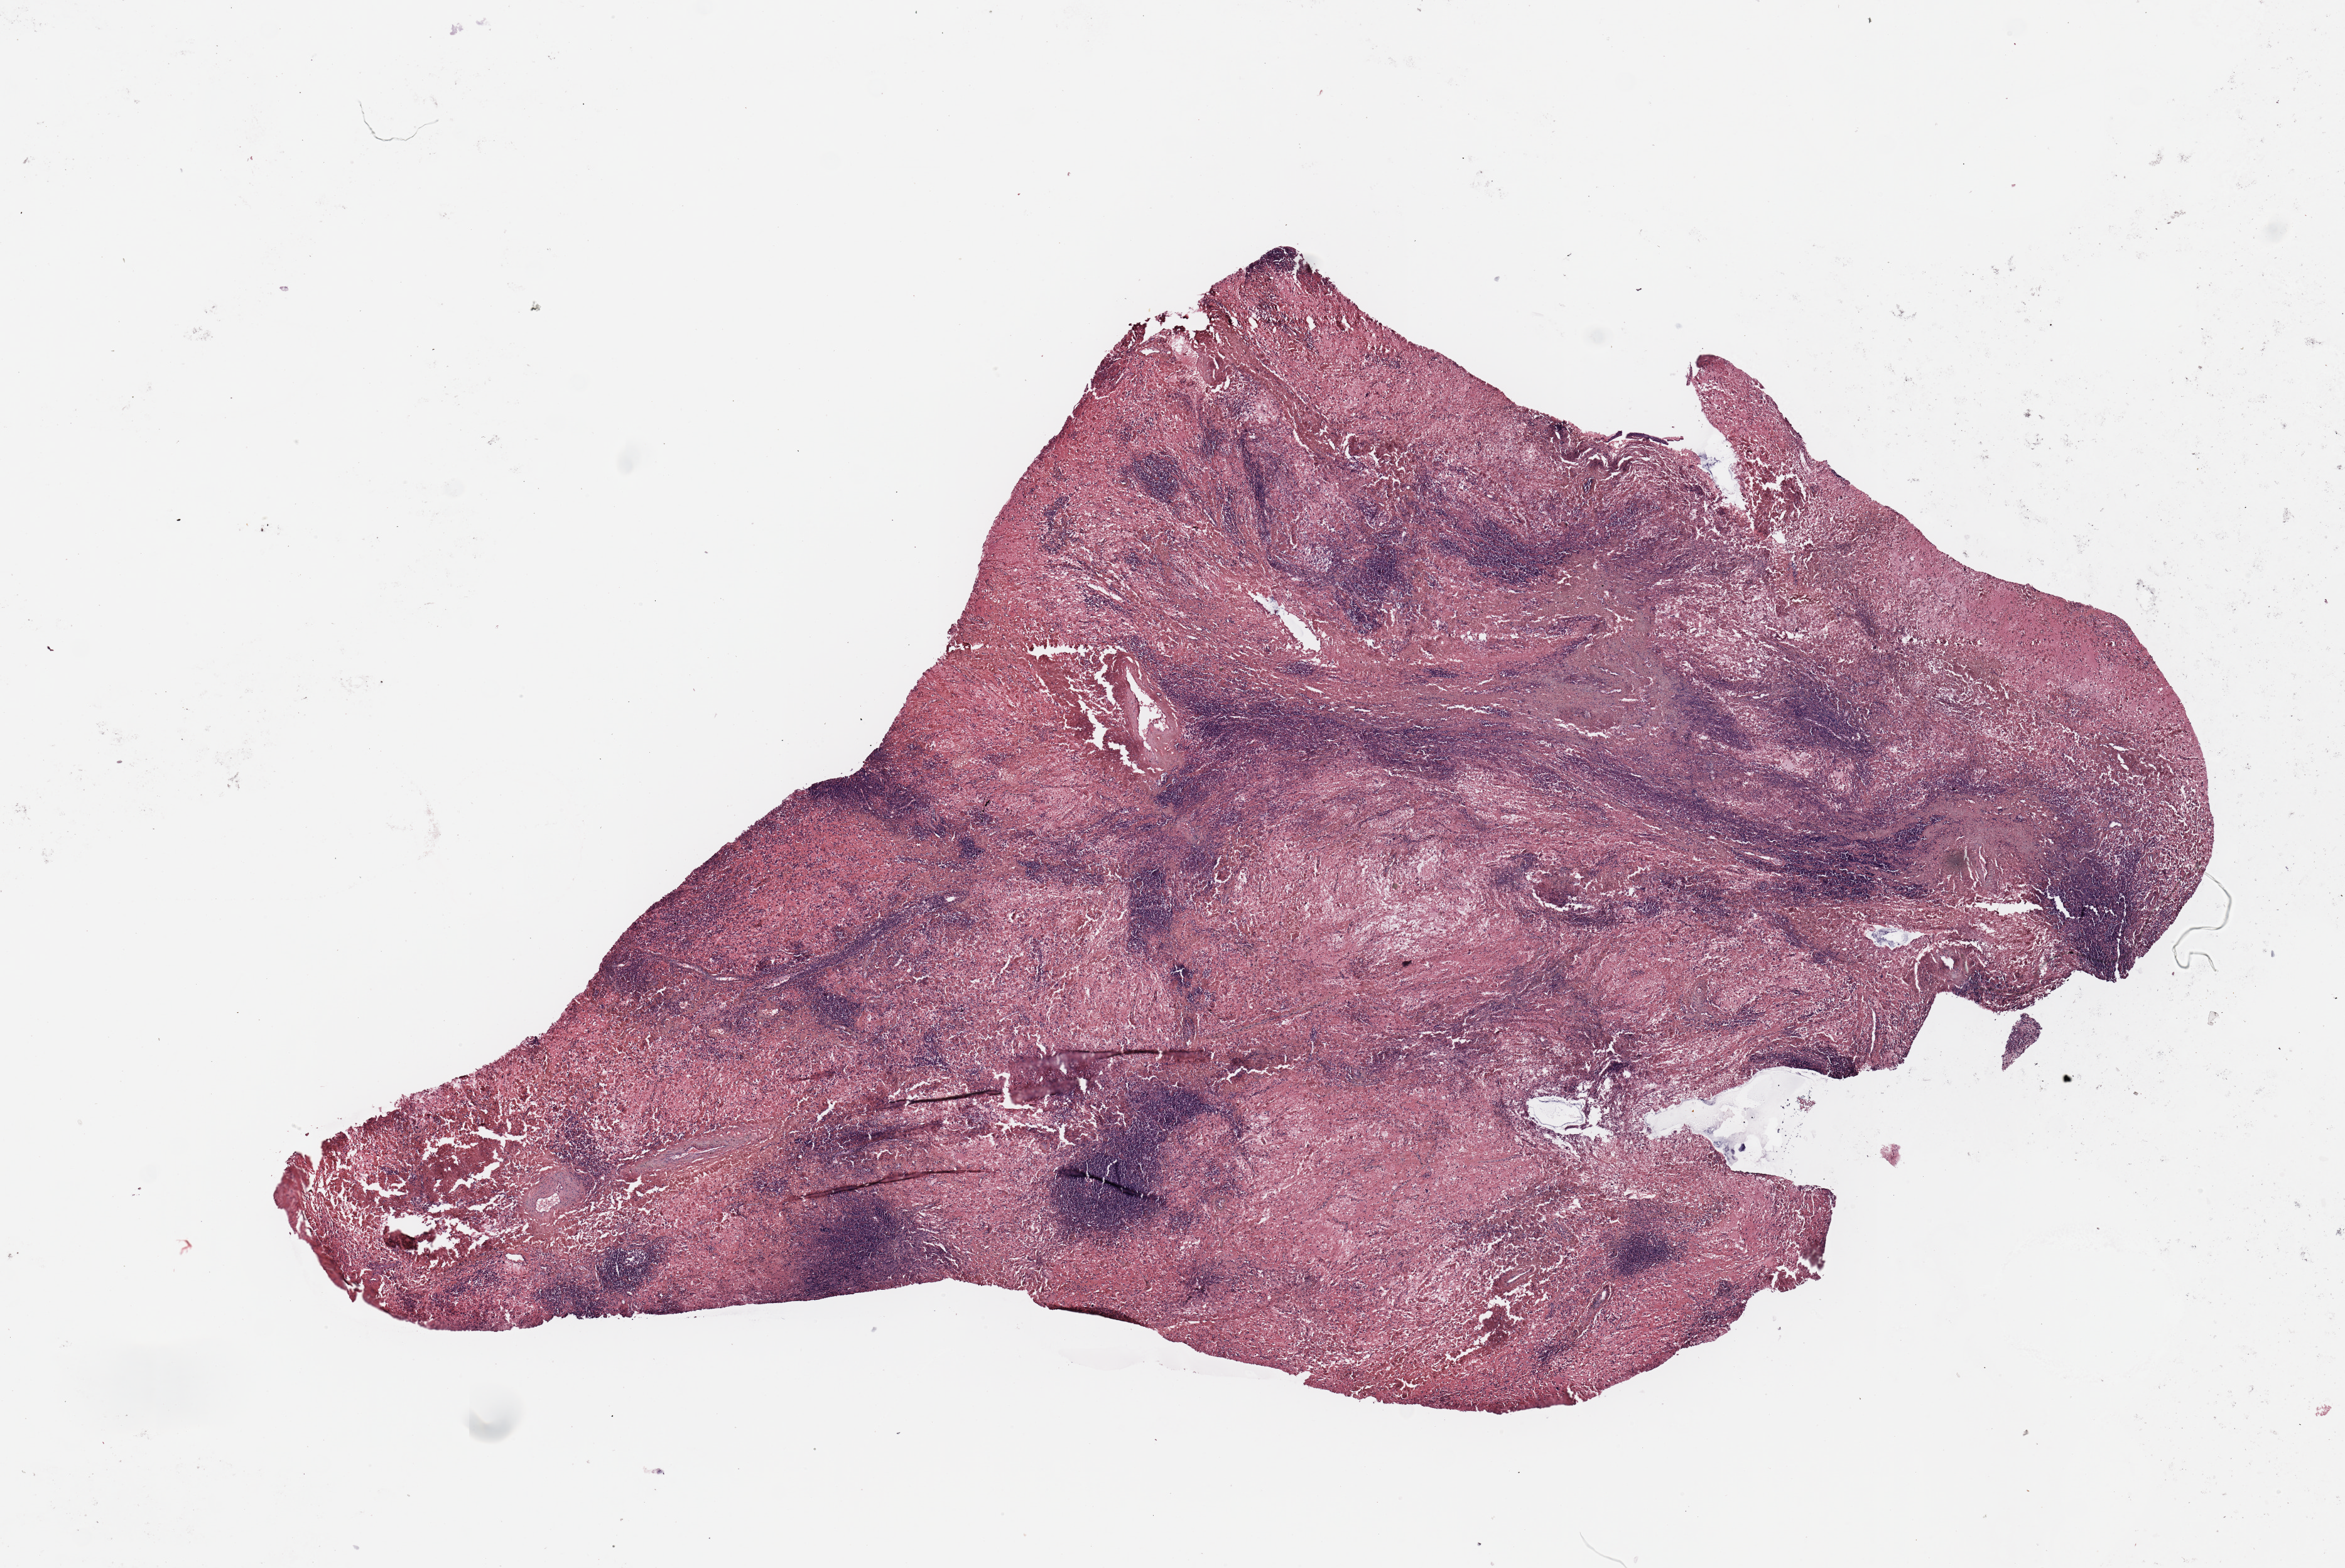
Digitized H&E-stained tissue section (whole slide), shown as a low-resolution overview of the whole scanned area (about 14.8 x 9.9 mm). Patient: male, age 64 years.
Patient diagnosis (cohort enrolment): sarcoma (site not recorded at cohort level).